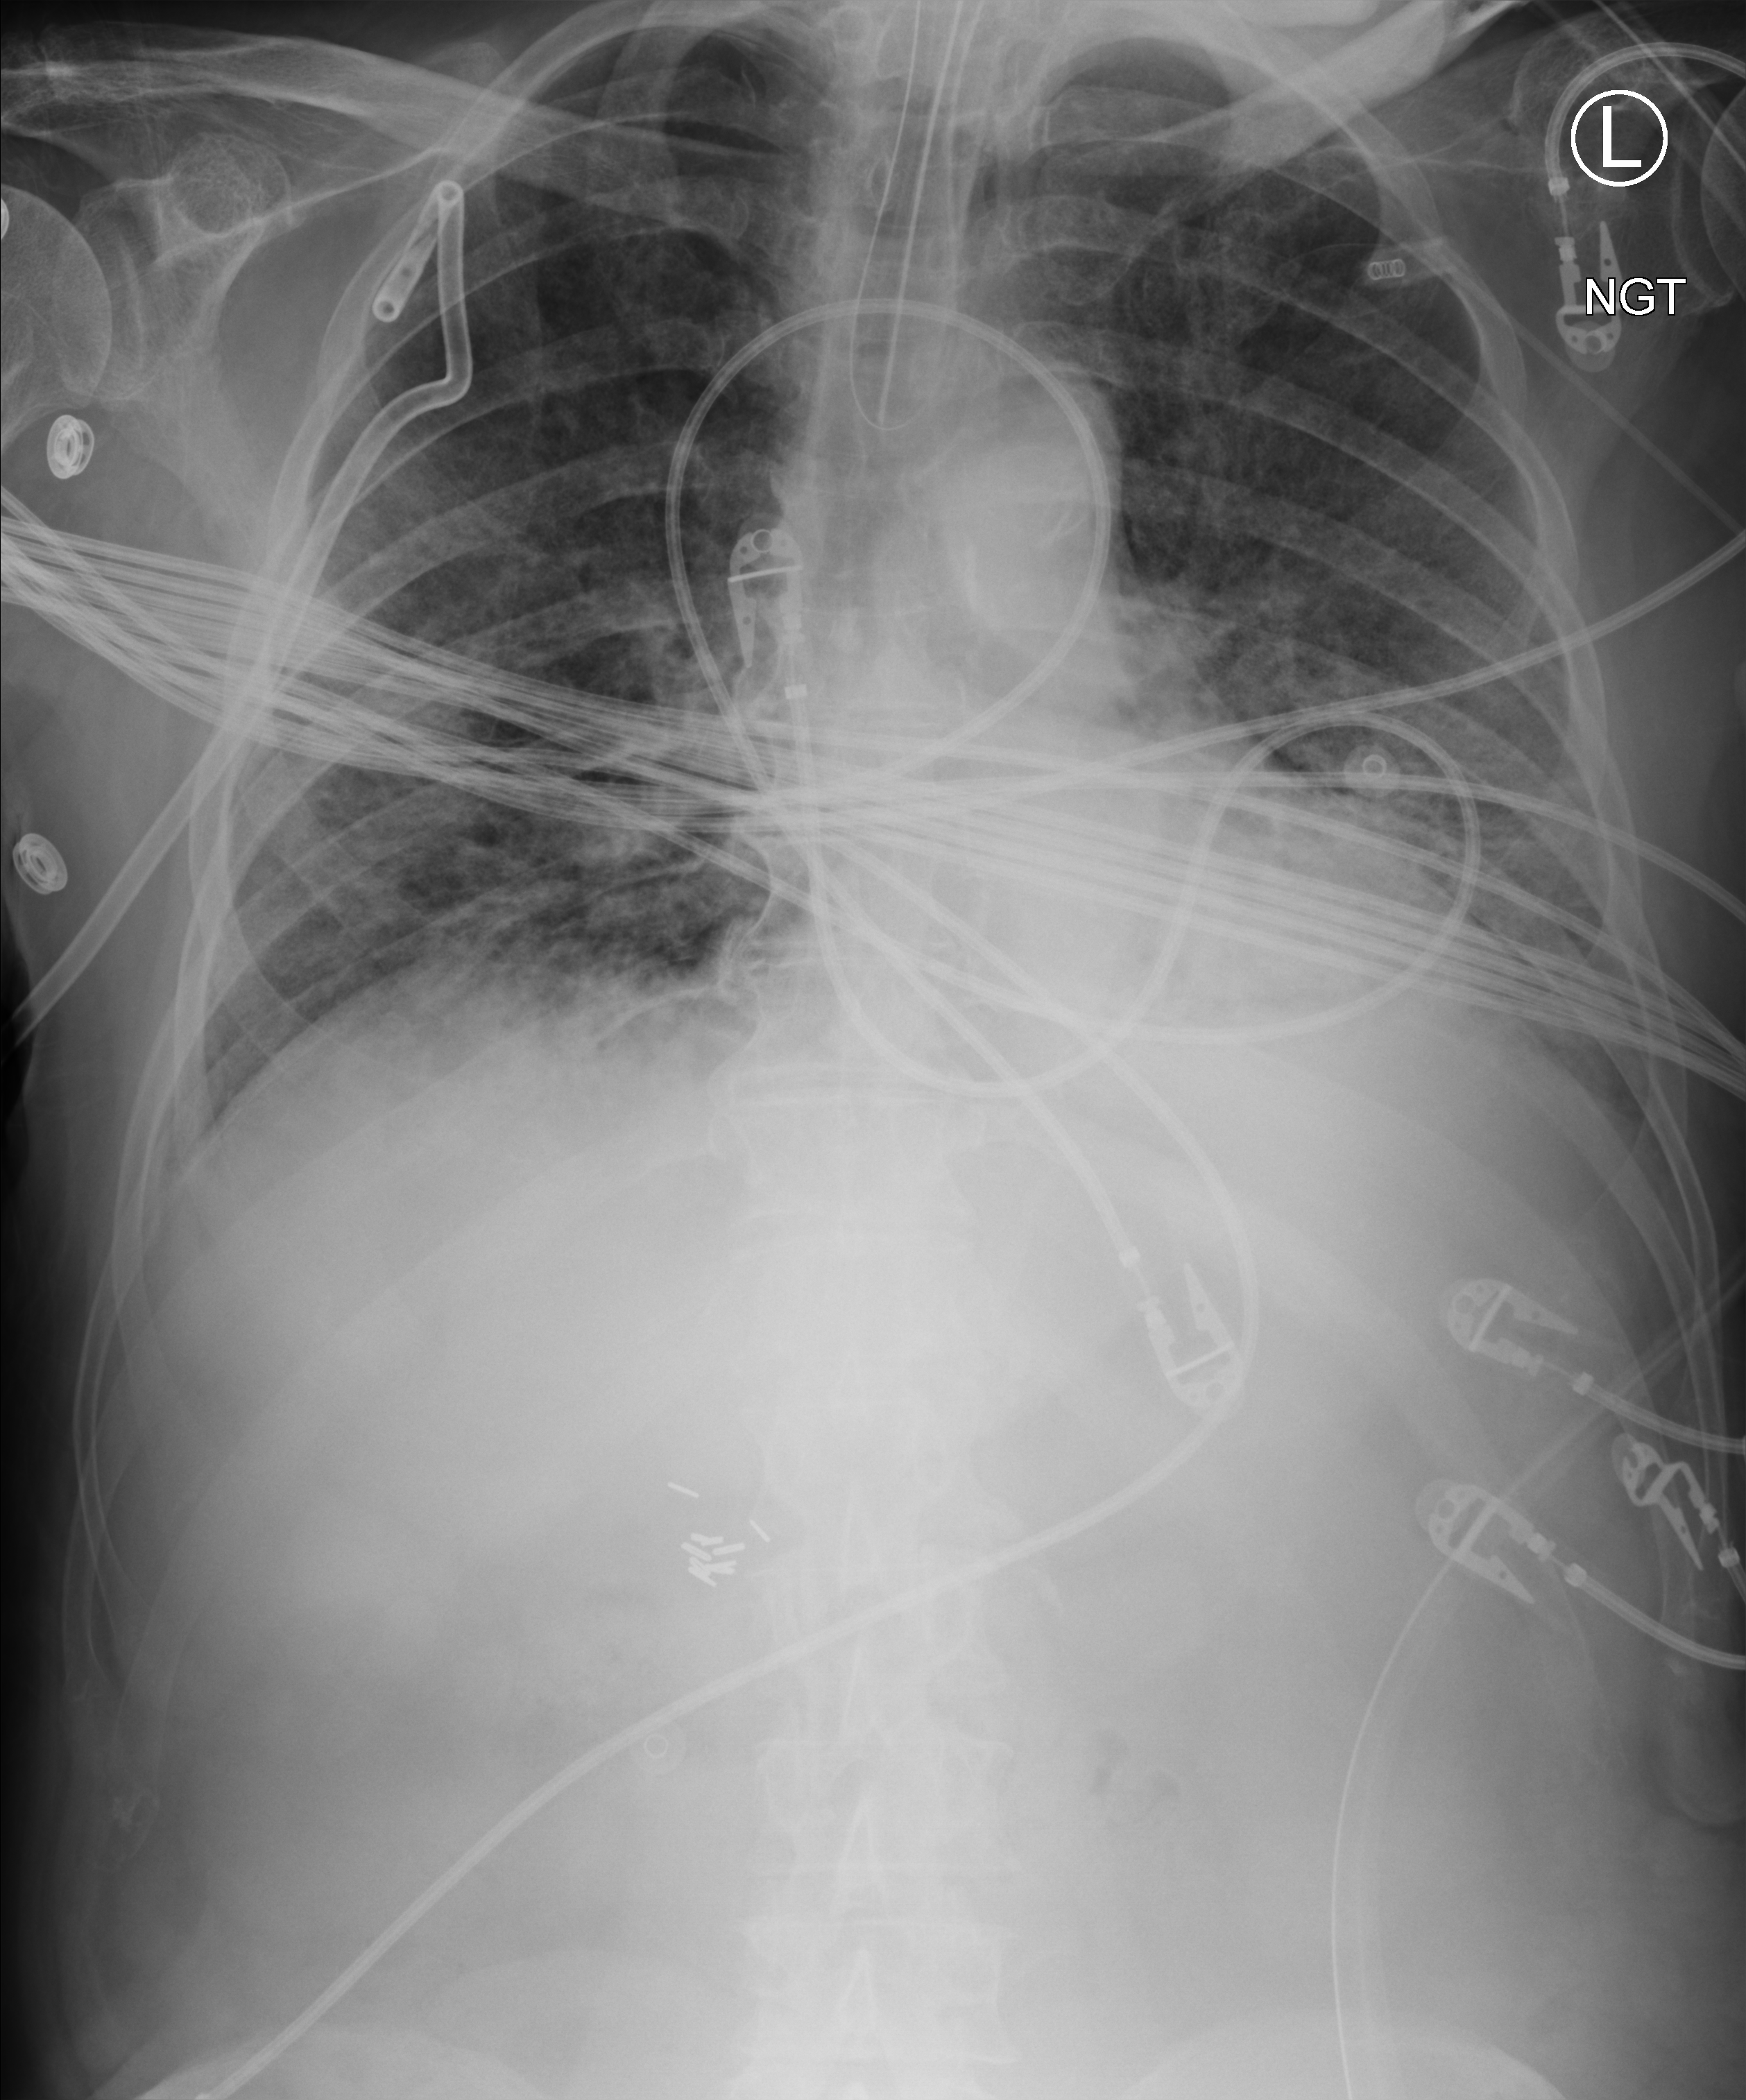
Bedside chest radiograph (computed radiography); anteroposterior (AP) projection. Male patient hospitalised with COVID-19, age 75–90 years.
Admission-level facts for this patient (not findings on this image; timing relative to this image not recorded): COPD (admission record): no.